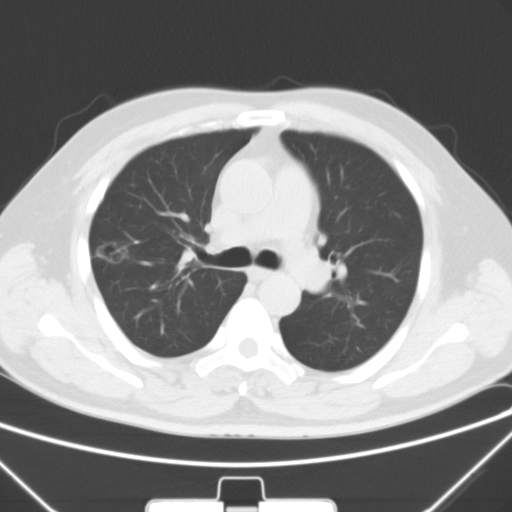
Chest CT, one axial slice. Slice 40 of 64 in the series (ordered by position). 120 kVp. Lung window (W 1500 / L -600 HU). 5 mm slice thickness. 512 × 512 image matrix, field of view 350 × 350 mm. Male patient, age 58 years. Case-level facts recorded for this patient, not image findings: clinical TNM (as recorded): T1c N0 M0; histopathological grade: G2.
Annotated regions visible in this slice (rectangle marked by the reading radiologist):
- lung tumour (recorded histology: adenocarcinoma): box from (x=95, y=230) to (x=134, y=274) px